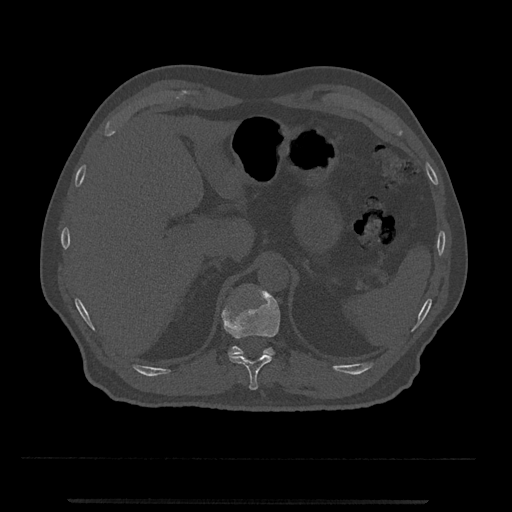
CT including the spine, one axial slice; slice 444 of 797 in the series (ordered by position); bone window (W 1800 / L 400 HU); 512 × 512 image matrix, field of view 419 × 419 mm. Patient: male, 63 years. From the clinical record (not read from this slice): primary cancer: prostate.
Annotated regions visible in this slice (semi-automatic segmentation, software-assisted and operator-edited):
- T11 vertebra: bounding box <222,288,280,390> (left, top, right, bottom; pixels)
- T12 vertebra: <228,346,275,356>